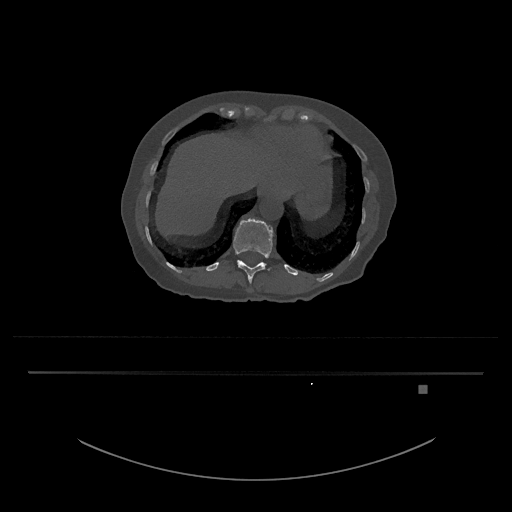
CT including the spine, one axial slice. Position 609 of 797 along the scan axis. Reconstruction kernel Br40s/3. 120 kVp. Bone window (W 1800 / L 400 HU). 512 × 512 image matrix. Patient: female, 57 years. From the clinical record (not read from this slice): primary cancer: cervical.
Annotated regions visible in this slice (semi-automatically segmented with operator editing):
- T12 vertebra: box from (x=233, y=218) to (x=274, y=284) px